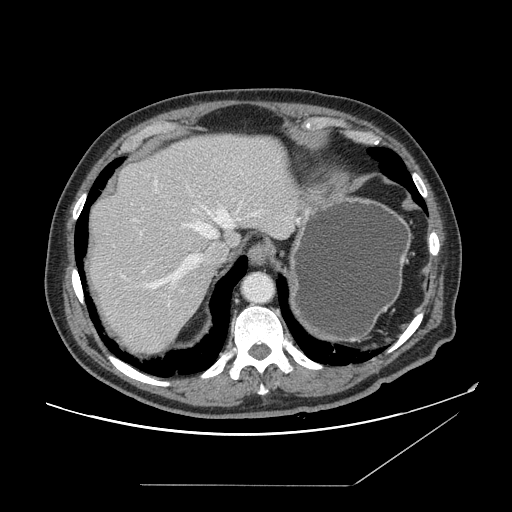
Contrast-enhanced abdominal CT, one axial slice; intravenous contrast given; soft-tissue window (W 400 / L 40 HU); 2.5 mm slice thickness; 512 × 512 image matrix, field of view 416 × 416 mm. Male patient, age 80 years. From the clinical record (not read from this slice): diagnosis: colorectal cancer liver metastases, imaged before liver resection; multiple liver metastases: no.
Annotated regions visible in this slice (manually delineated by an expert):
- hepatic veins: bounding box <146,184,261,288> (left, top, right, bottom; pixels)
- liver: <88,135,296,353>
- planned liver remnant (the part of the liver to remain after resection): <89,135,297,256>
- portal vein (with intrahepatic branches): <141,209,196,273>